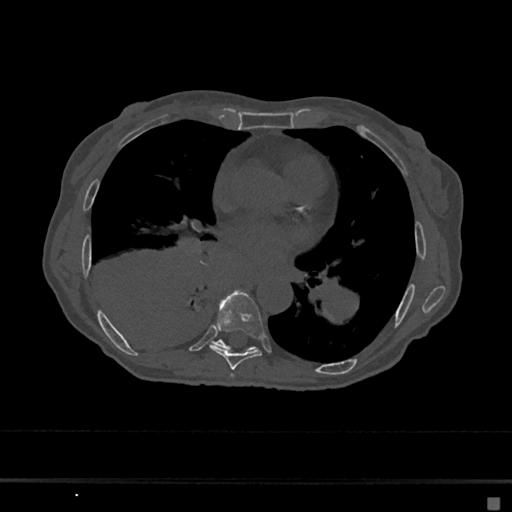
CT including the spine, one axial slice. Position 358 of 797 along the scan axis. Reconstruction kernel Br40s/3. 120 kVp. Bone window (W 1800 / L 400 HU). 0.5 mm slice thickness. 512 × 512 image matrix, field of view 360 × 360 mm. Patient: female, 68 years. Case-level facts recorded for this patient, not image findings: primary cancer: renal.
Outlined on this slice (semi-automatically segmented with operator editing):
- T6 vertebra: bounding box (x1, y1, x2, y2) in pixels: (230, 374, 234, 378)
- T7 vertebra: (210, 291, 264, 370)
- T8 vertebra: (213, 340, 255, 351)